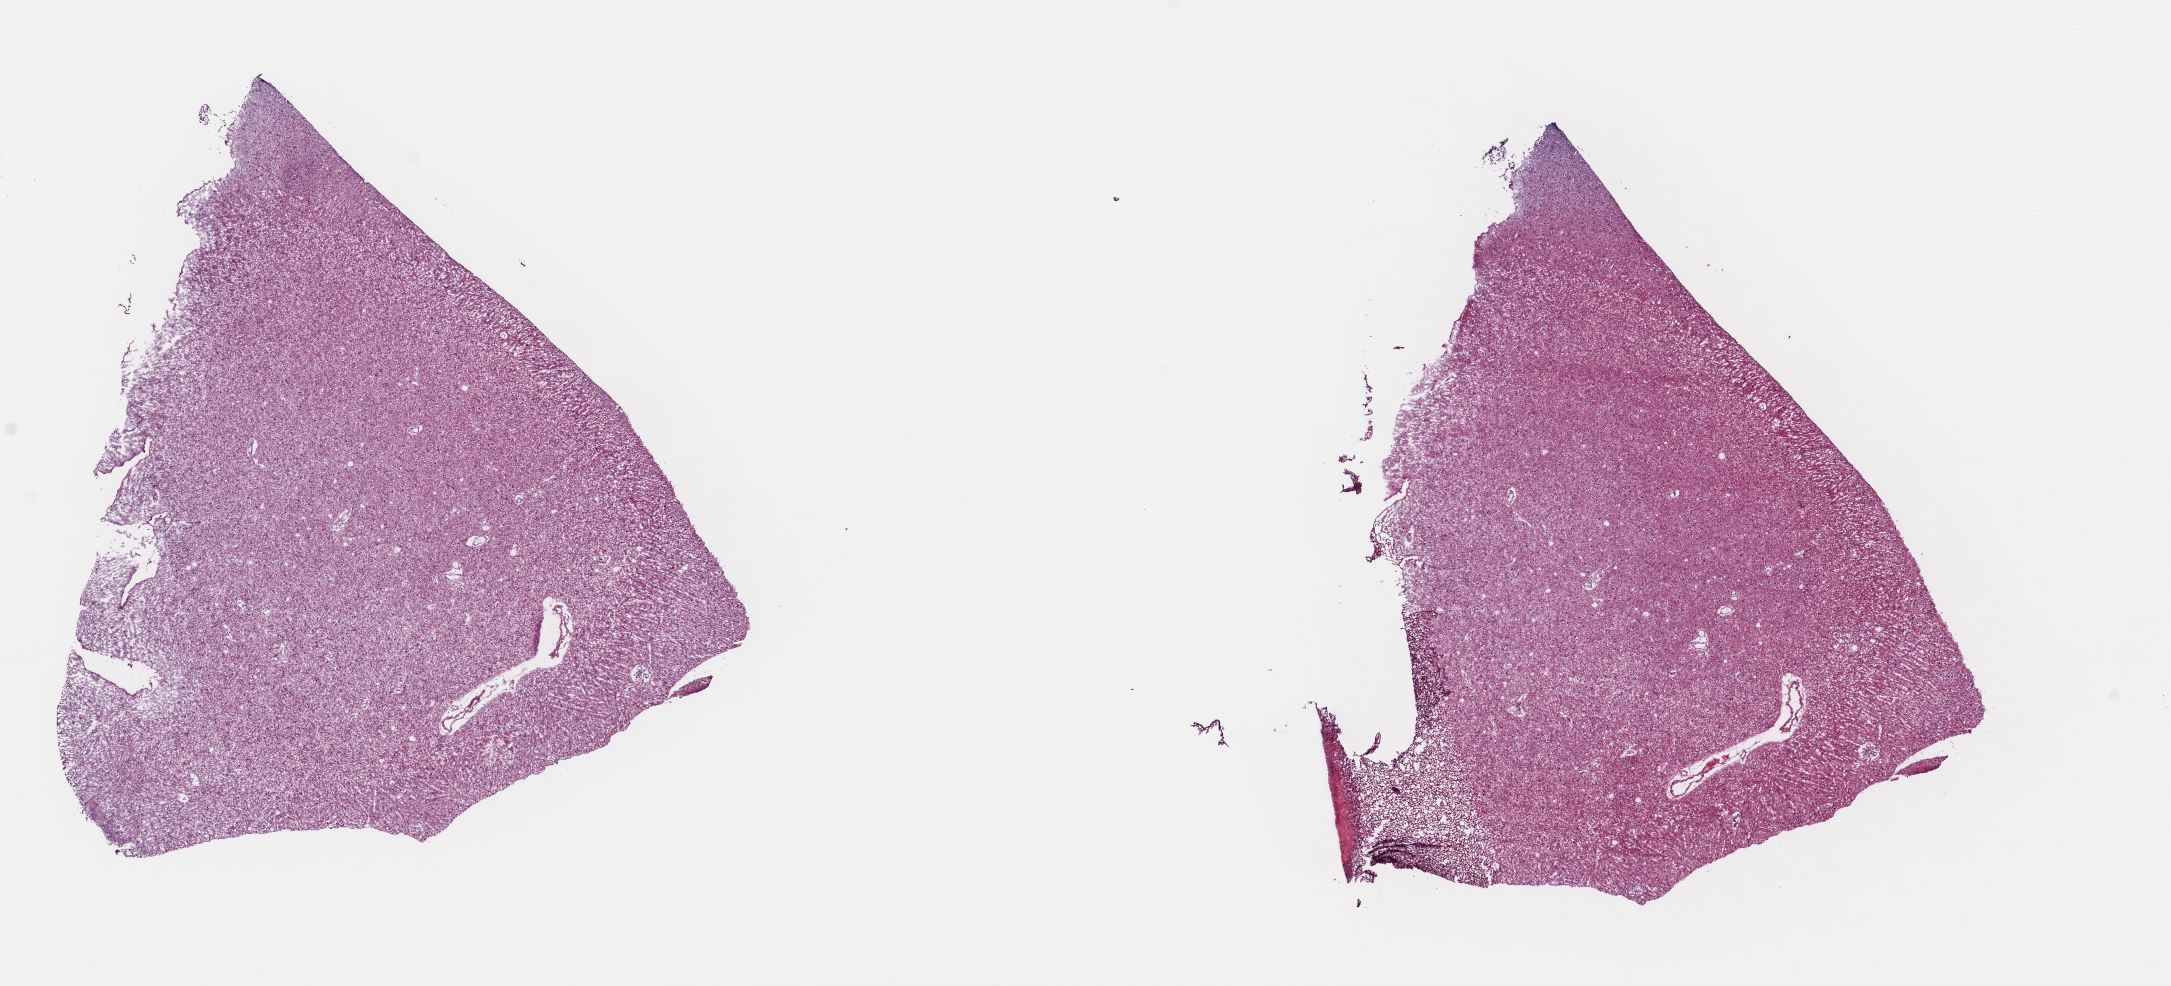
Digitized H&E tissue section (whole slide), whole scanned area (about 17.2 x 7.8 mm, slide scanned at 40x) shown as a low-resolution overview. Frozen section. Sample: primary tumour, brain. Male, age 54 years at initial diagnosis. Histologic grade: G2 (moderately differentiated). Pathologist review of this section (percent, as recorded): tumour cells 60%, tumour nuclei 75%, normal cells 10%, stromal cells 30%, necrosis 0%. Inflammatory infiltration, as recorded: lymphocyte infiltration 0%, monocyte infiltration 5%, neutrophil infiltration 0%.
Pathologic diagnosis: Oligodendroglioma, NOS.